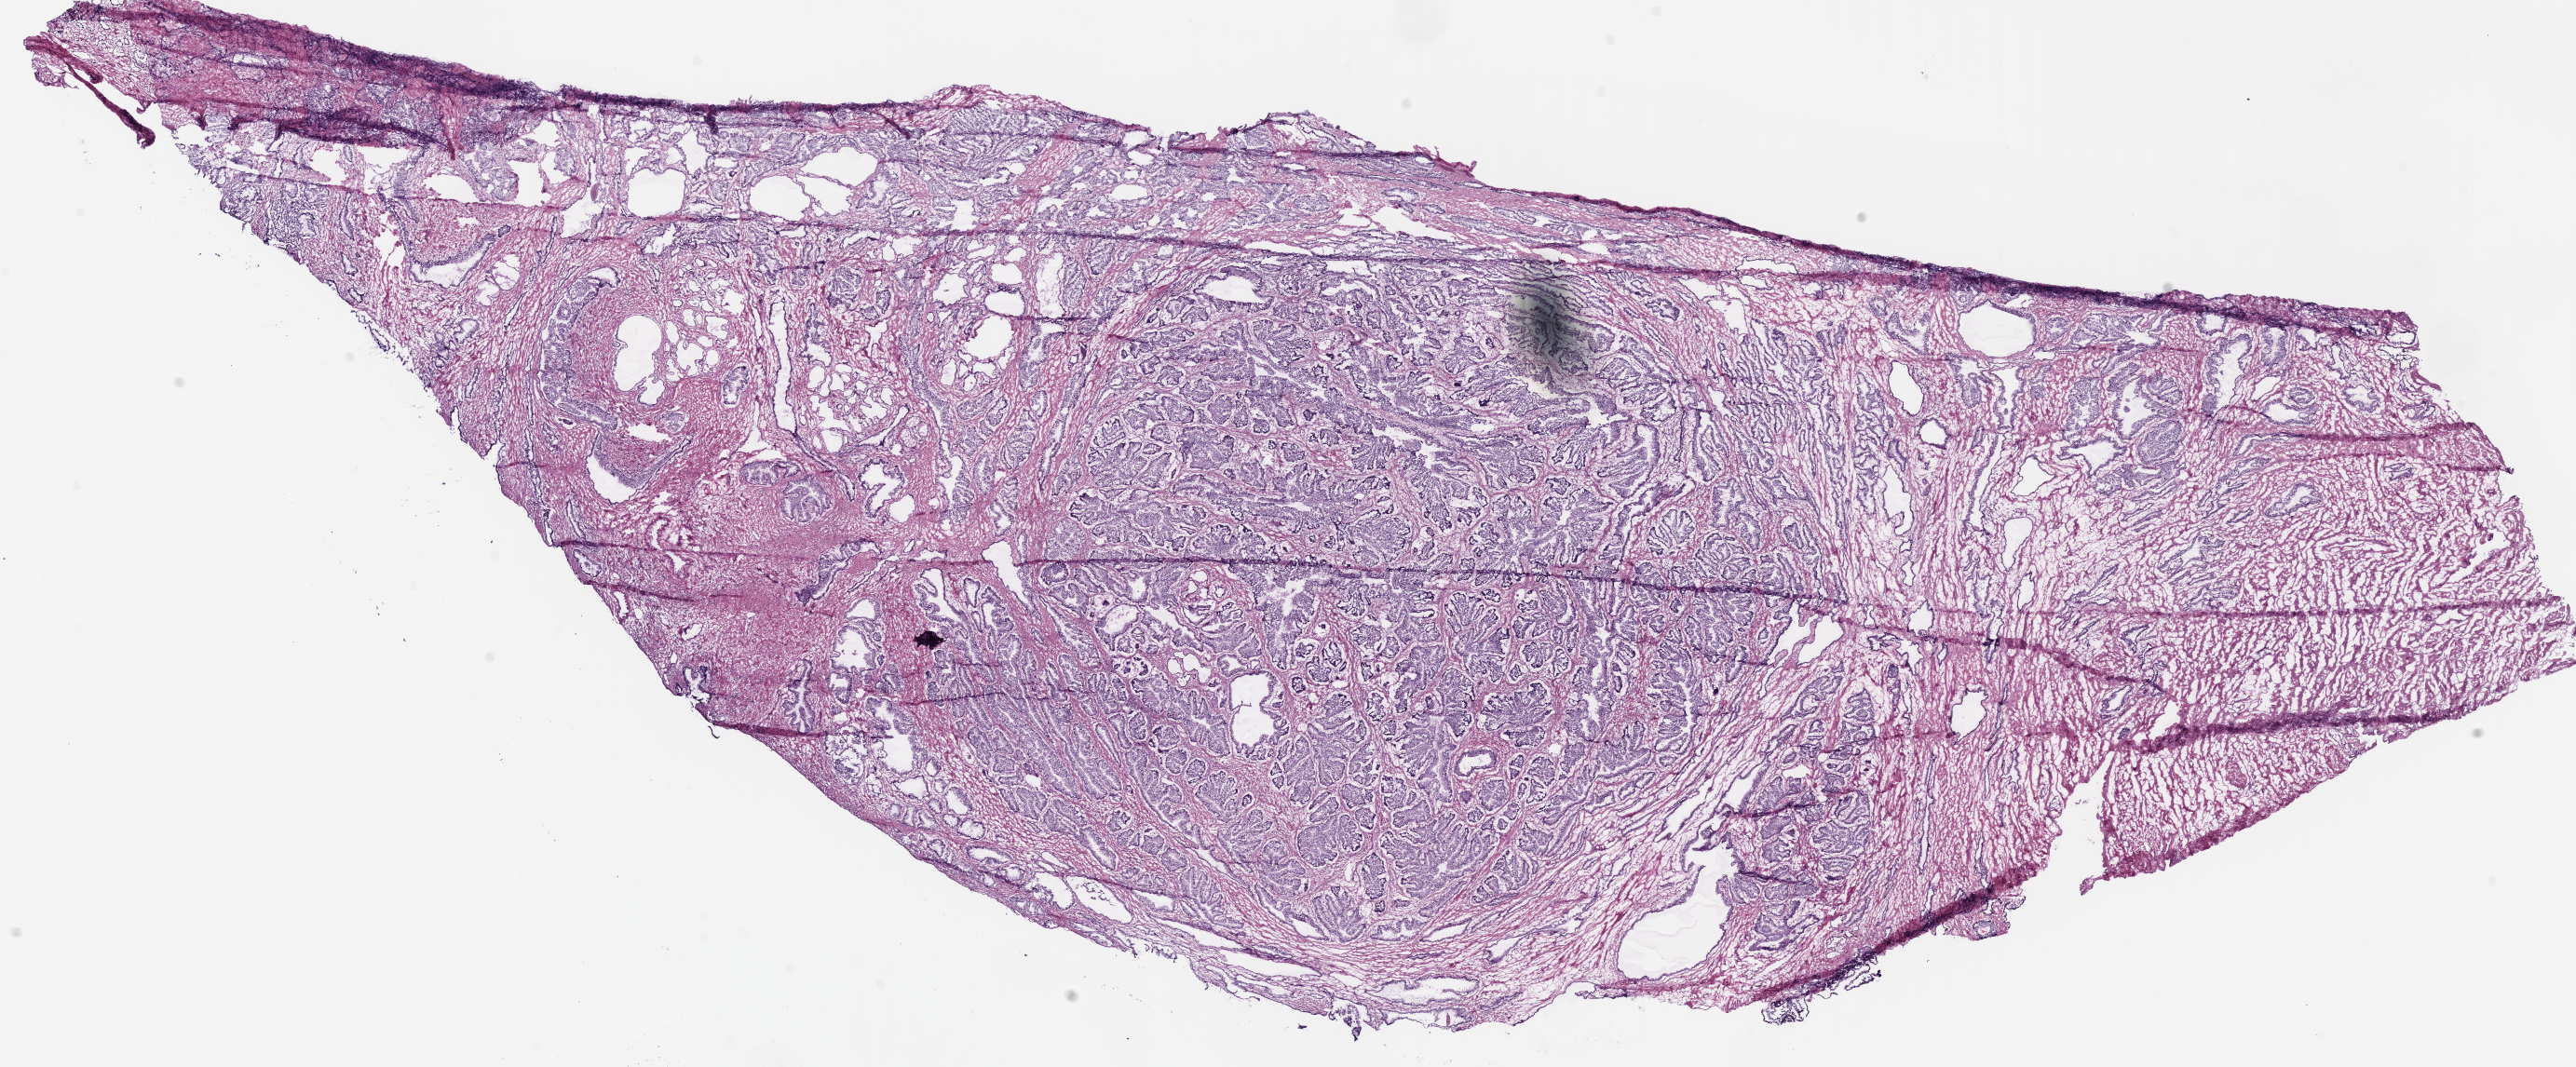
Digitized H&E-stained tissue section (whole slide) — a low-resolution overview of the entire scanned area, about 21.8 x 9.0 mm (from a 40x scan), frozen section, sample: solid tissue normal (non-tumour tissue), prostate. Male, age 61 years at initial diagnosis.
This section: solid tissue normal sample (biorepository sample class). Patient diagnosis: Acinar cell carcinoma (prostate gland).